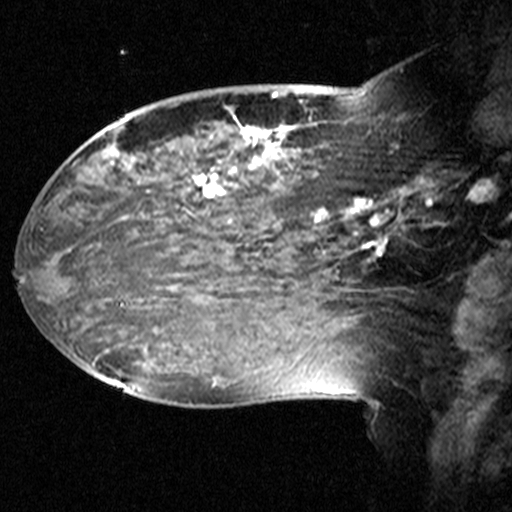
Breast MRI (dynamic contrast-enhanced), one sagittal slice. Slice 19 of 44 in the series (ordered by position). Dynamic contrast-enhanced study with each time point stored as its own series, time point 2 of 3 at this slice position (early post-contrast, ordered by acquisition time). 1.5 T. TE 4.5 ms, TR 11 ms. 512 × 512 image matrix, field of view 240 × 240 mm. Patient: female, 38 years. Case-level facts recorded for this patient, not image findings: setting: breast cancer imaged before/during neoadjuvant chemotherapy; receptor status: HR-positive, HER2-negative.
Structures marked on this image (semi-automatically segmented with operator editing):
- analysis volume of interest (the breast-tissue region the enhancement analysis was run in; not a lesion): bounding box (x1, y1, x2, y2) in pixels: (124, 106, 405, 245)
- tumour enhancement mask (voxels above the 90 % enhancement threshold inside the analysis volume of interest): (196, 107, 388, 243)